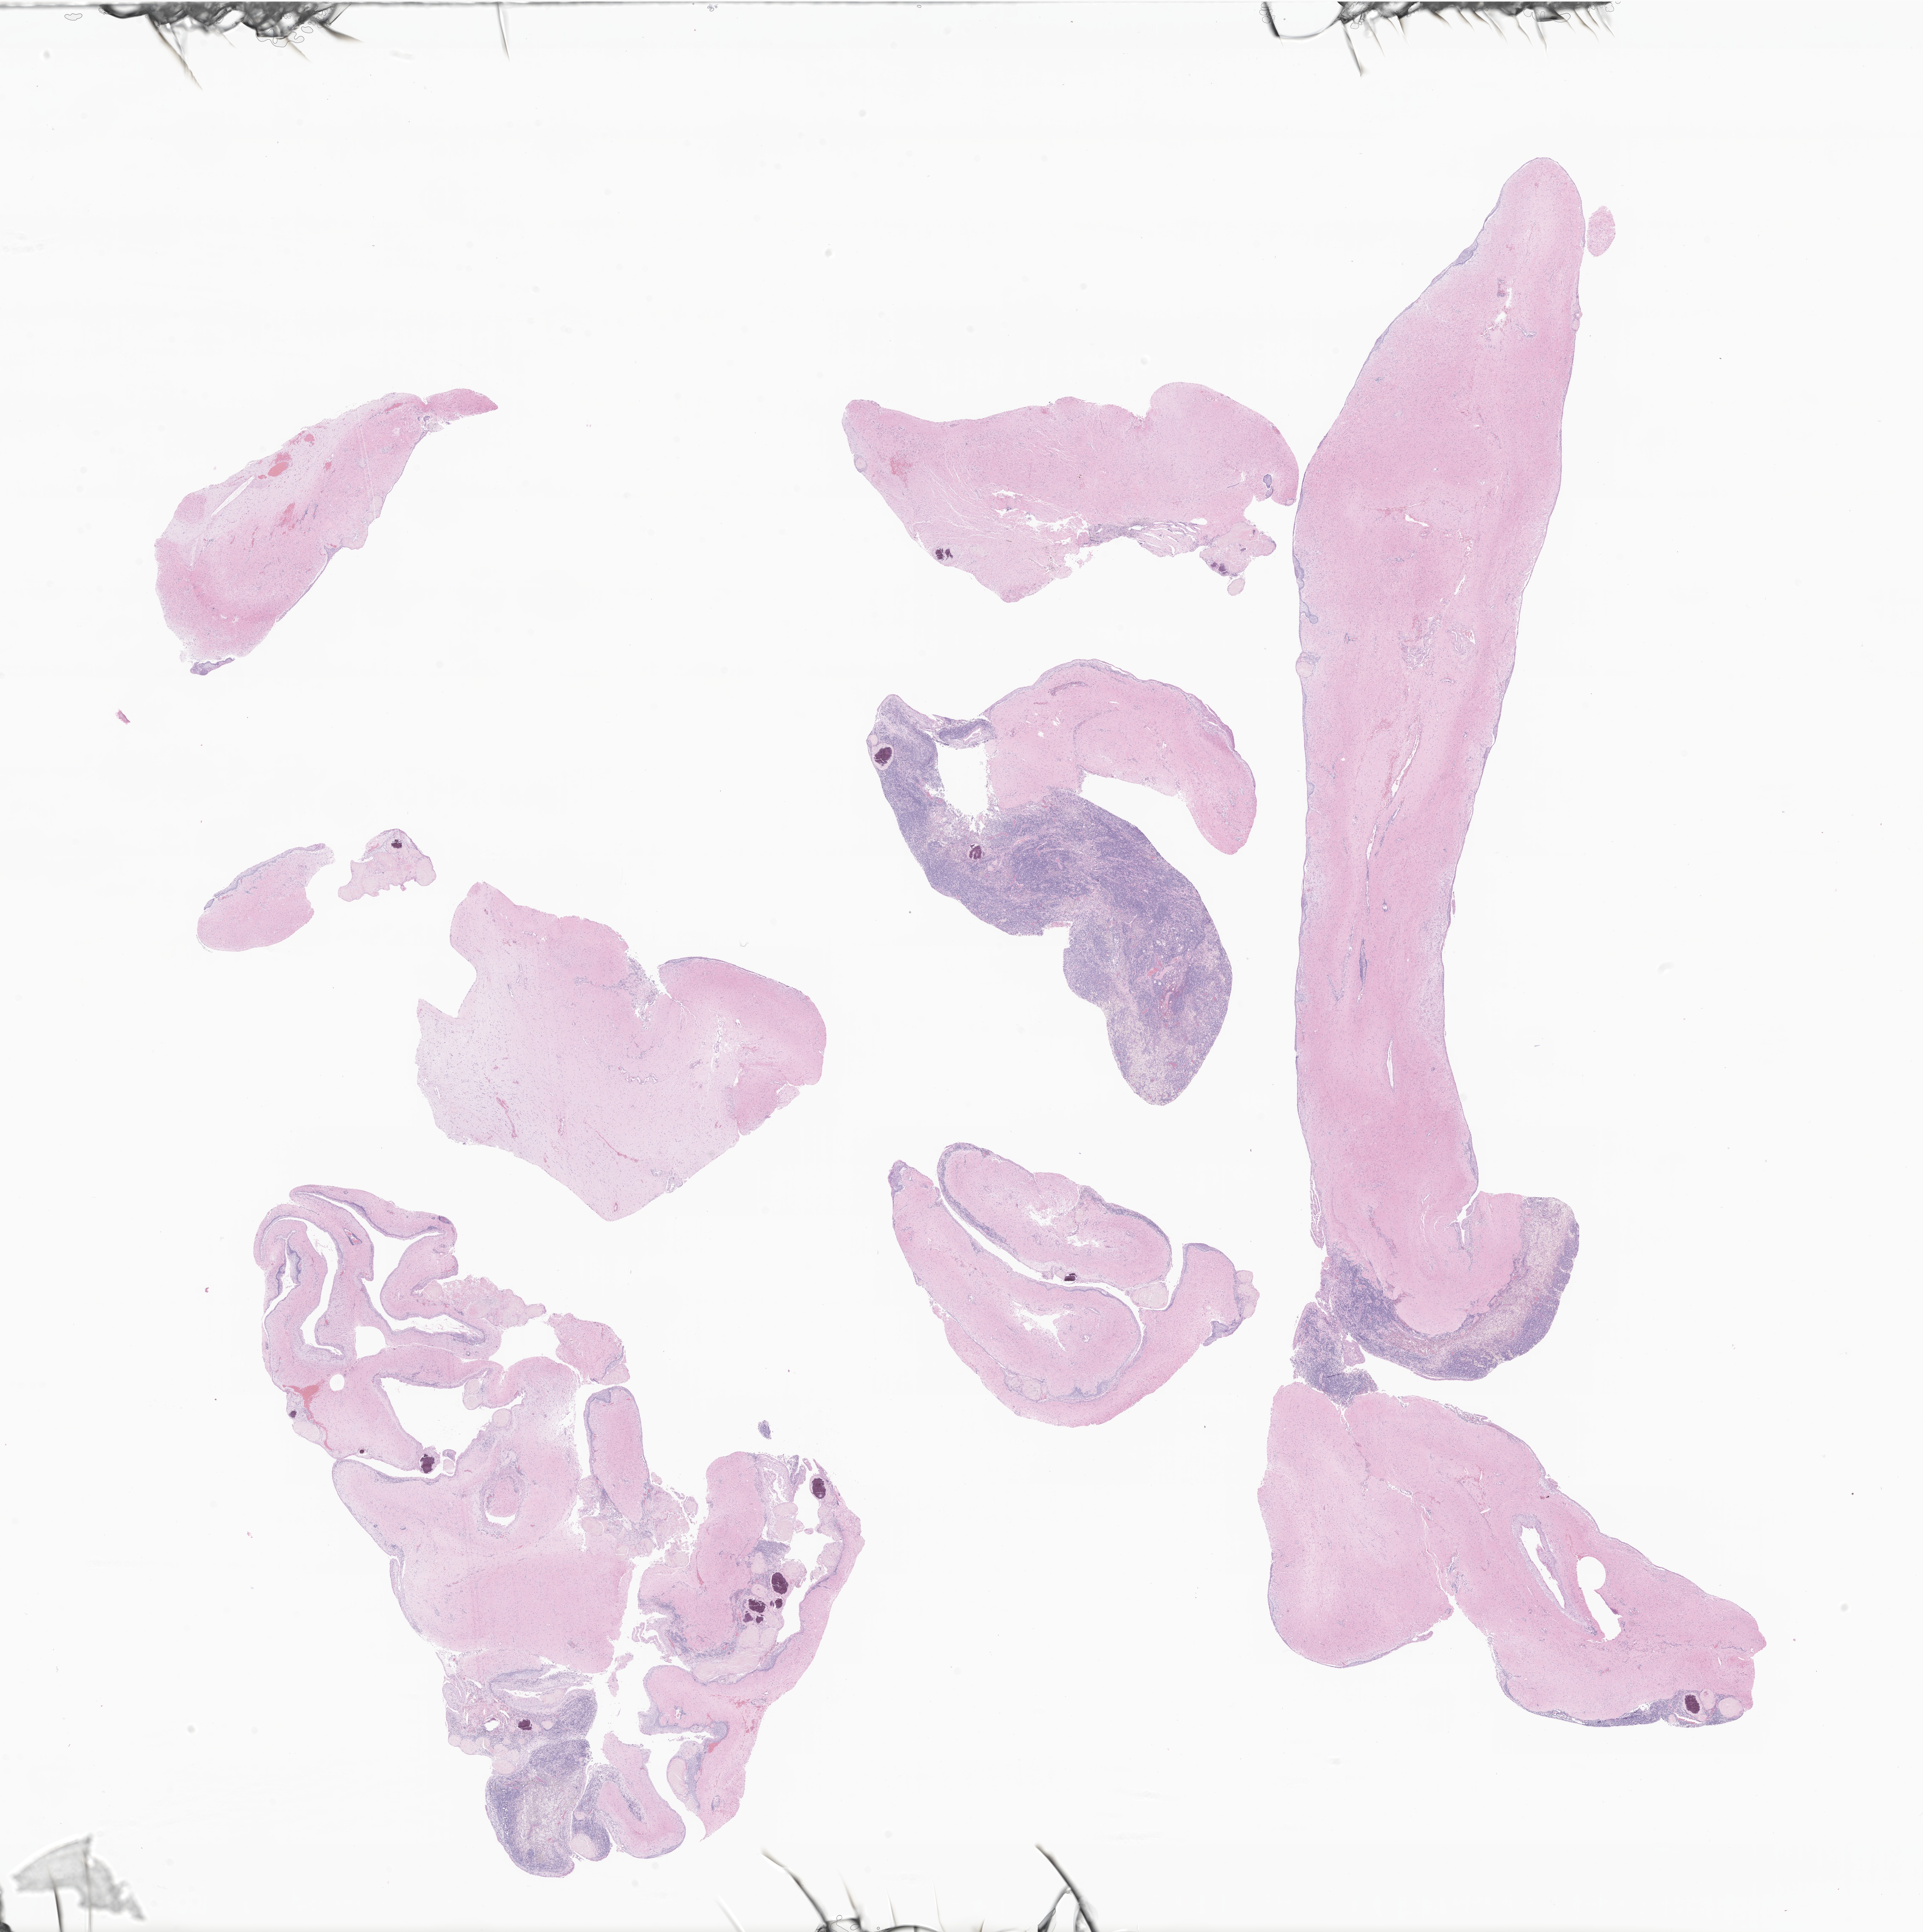
H&E whole-slide image of tumor tissue from the brain — whole scanned area (about 22.9 x 23.0 mm) shown as a low-resolution overview. Formalin-fixed, paraffin-embedded (FFPE) tissue. Patient: female, age 141 months (11 years 9 months).
- recorded diagnosis: Craniopharyngioma, adamantinomatous